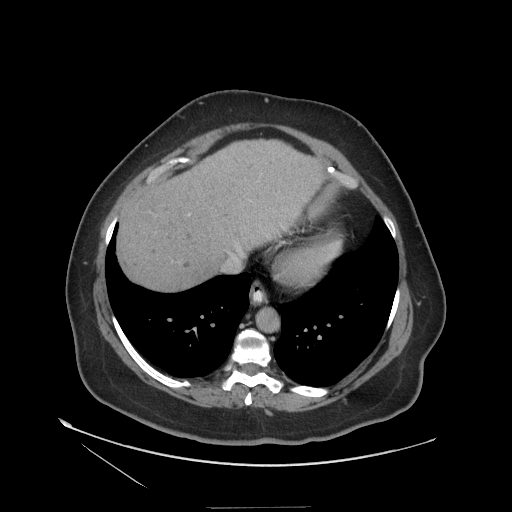
Contrast-enhanced abdominal CT (liver protocol), one axial slice; slice 101 of 127 in the series (ordered by position); reconstruction kernel STANDARD; 140 kVp; soft-tissue window (W 400 / L 40 HU); 512 × 512 image matrix, field of view 480 × 480 mm. From the clinical record (not read from this slice): diagnosis: hepatocellular carcinoma (patient treated with transarterial chemoembolisation; whether this scan precedes or follows treatment is not stated here); TNM stage (as recorded): Stage-II; Child-Pugh class: A; tumour differentiation: well differentiated; tumour nodularity: multinodular.
Annotated regions visible in this slice (semi-automatic segmentation, software-assisted and operator-edited):
- liver parenchyma outside the tumour (the mass and vessels are separate outlines, so this box may not span the whole liver): bounding box [x1, y1, x2, y2] px = [116, 140, 326, 290]